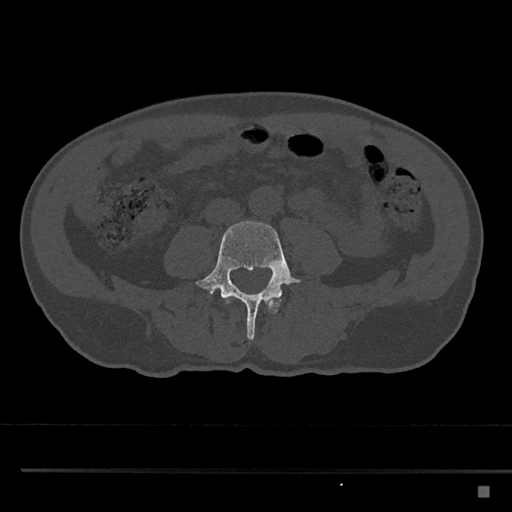
CT including the spine, one axial slice; position 639 of 797 along the scan axis; reconstruction kernel Br40s/3; 120 kVp; bone window (W 1800 / L 400 HU); 512 × 512 image matrix, field of view 391 × 391 mm. Male patient, age 59 years. Case-level facts recorded for this patient, not image findings: primary cancer: prostate.
Structures marked on this image (semi-automatically segmented with operator editing):
- L3 vertebra: bounding box (x1, y1, x2, y2) in pixels: (224, 296, 281, 313)
- L4 vertebra: (196, 221, 300, 340)
- L5 vertebra: (206, 289, 211, 296)